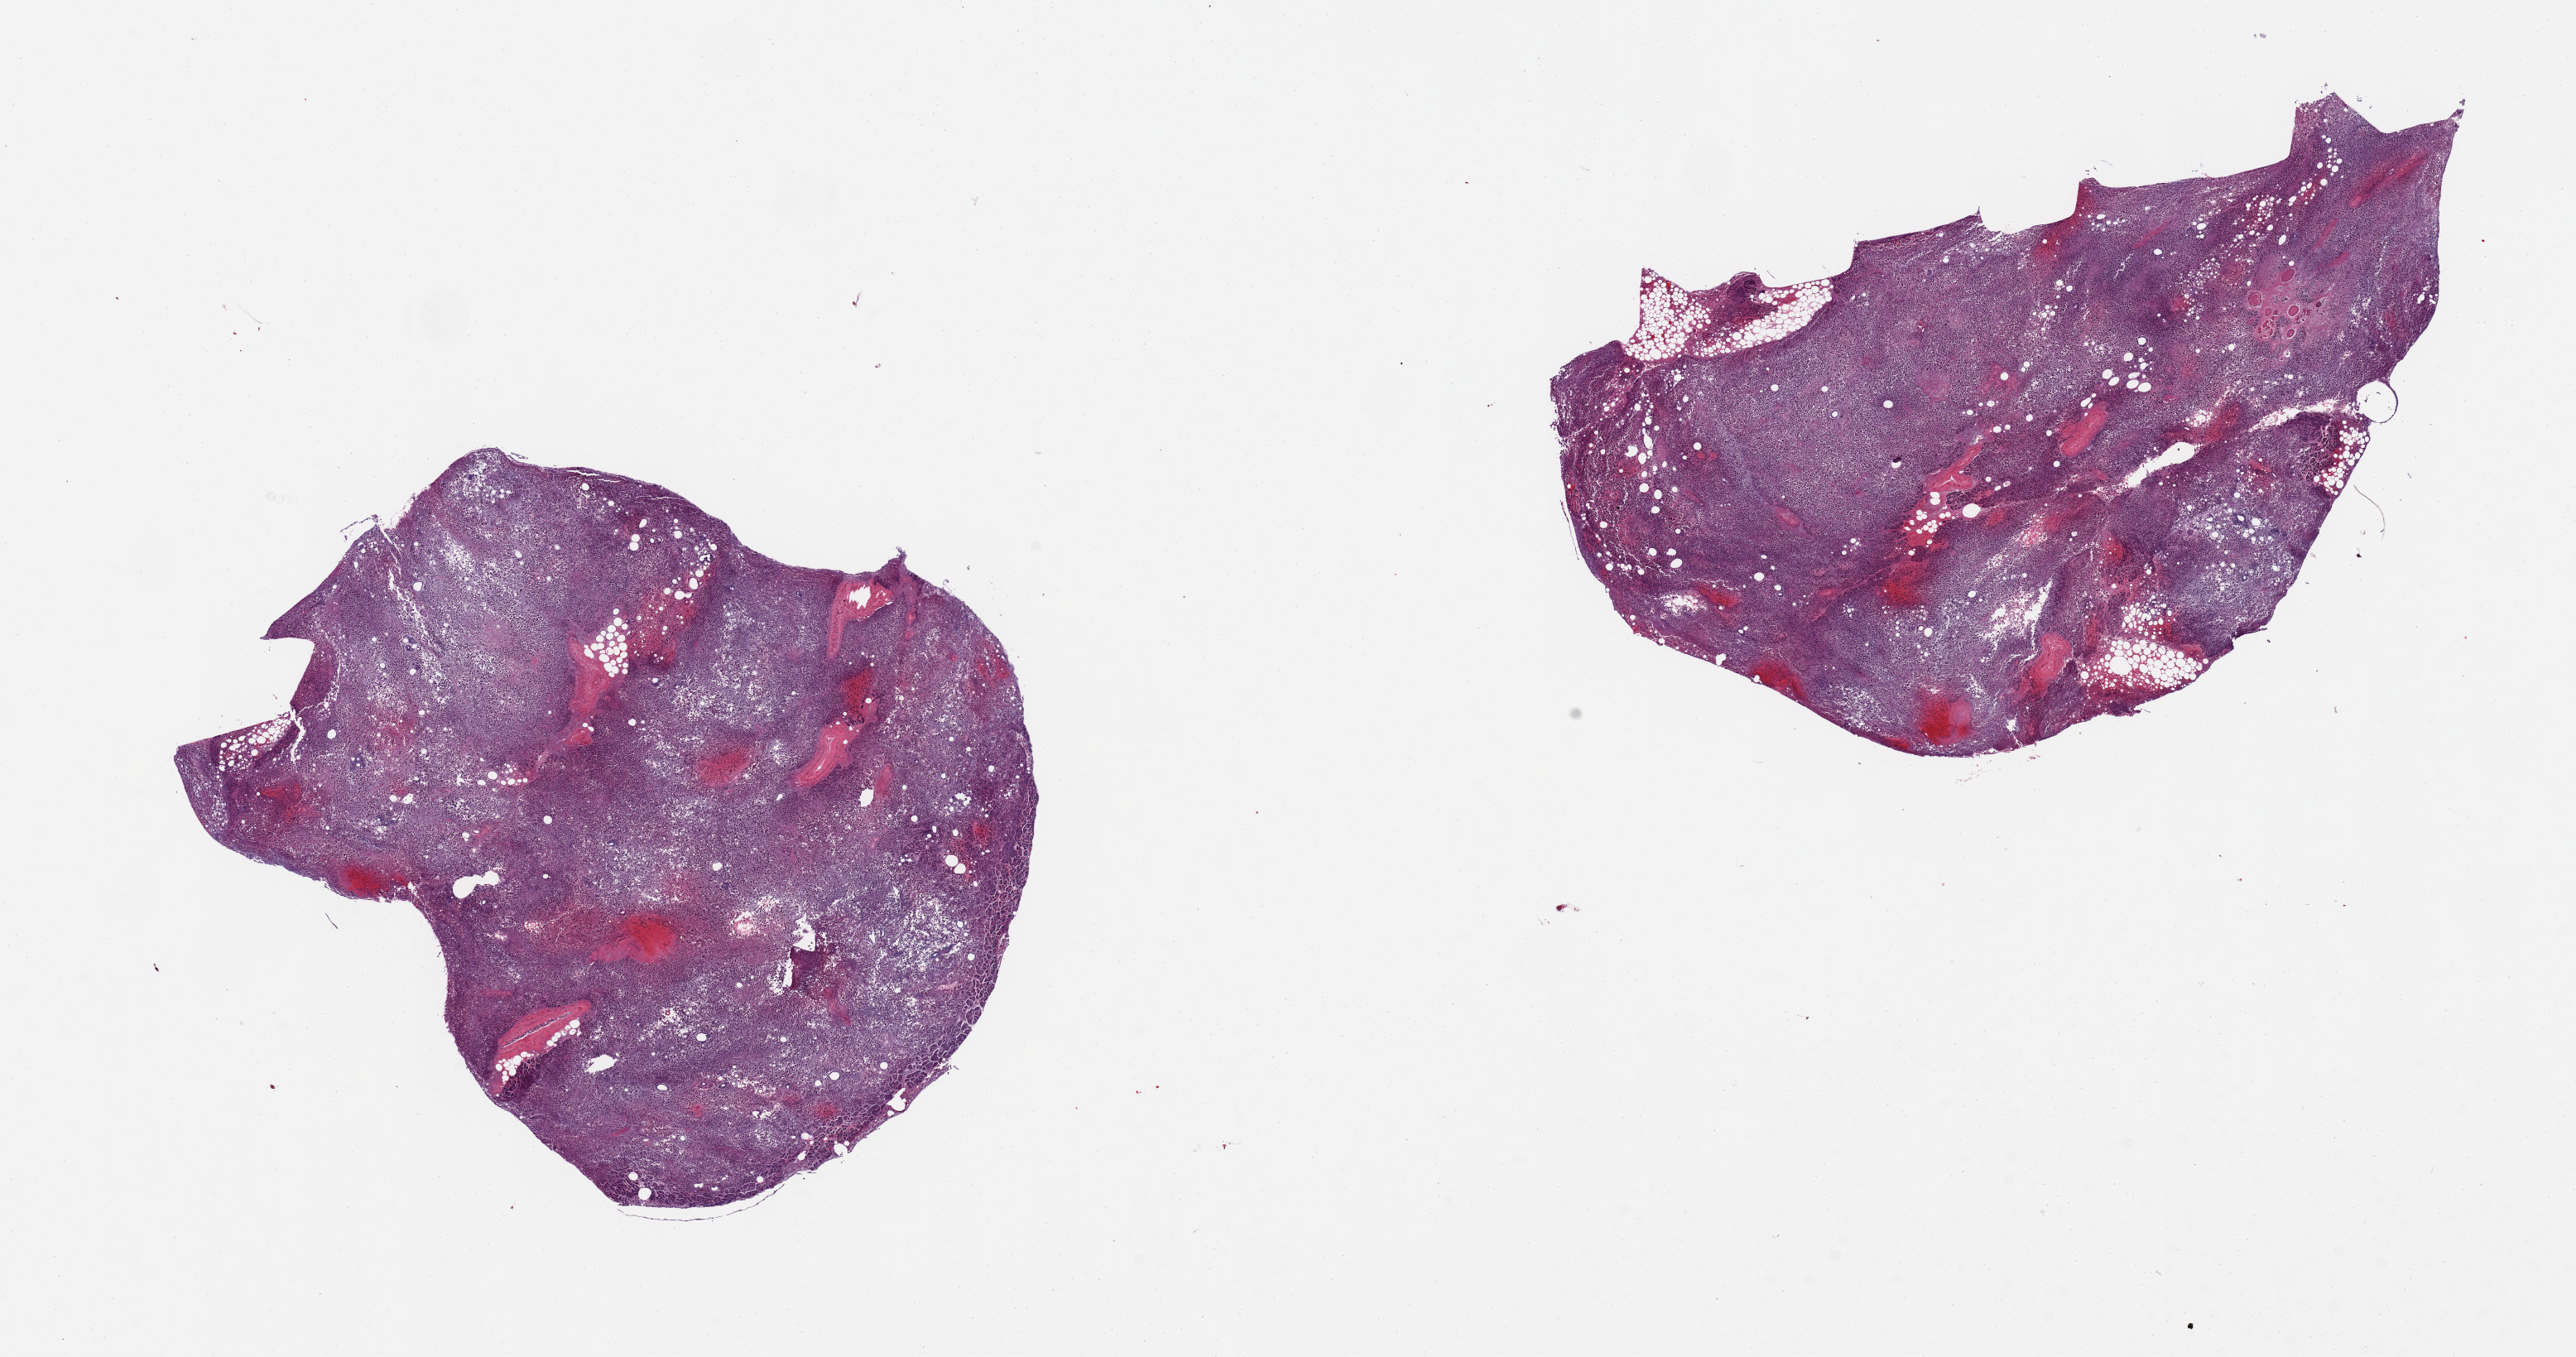
Digitized haematoxylin and eosin-stained section, low-resolution overview of the scanned area, about 24.6 x 13.0 mm. PAXgene-fixed, paraffin-embedded tissue. Sampled site (target tissue): pancreas. Donor tissue sample. Donor sex: male.
- pathologist's review note for this sample: 2 pieces, markedly autolyzed pancreas (not adipose tissue as initially designated)